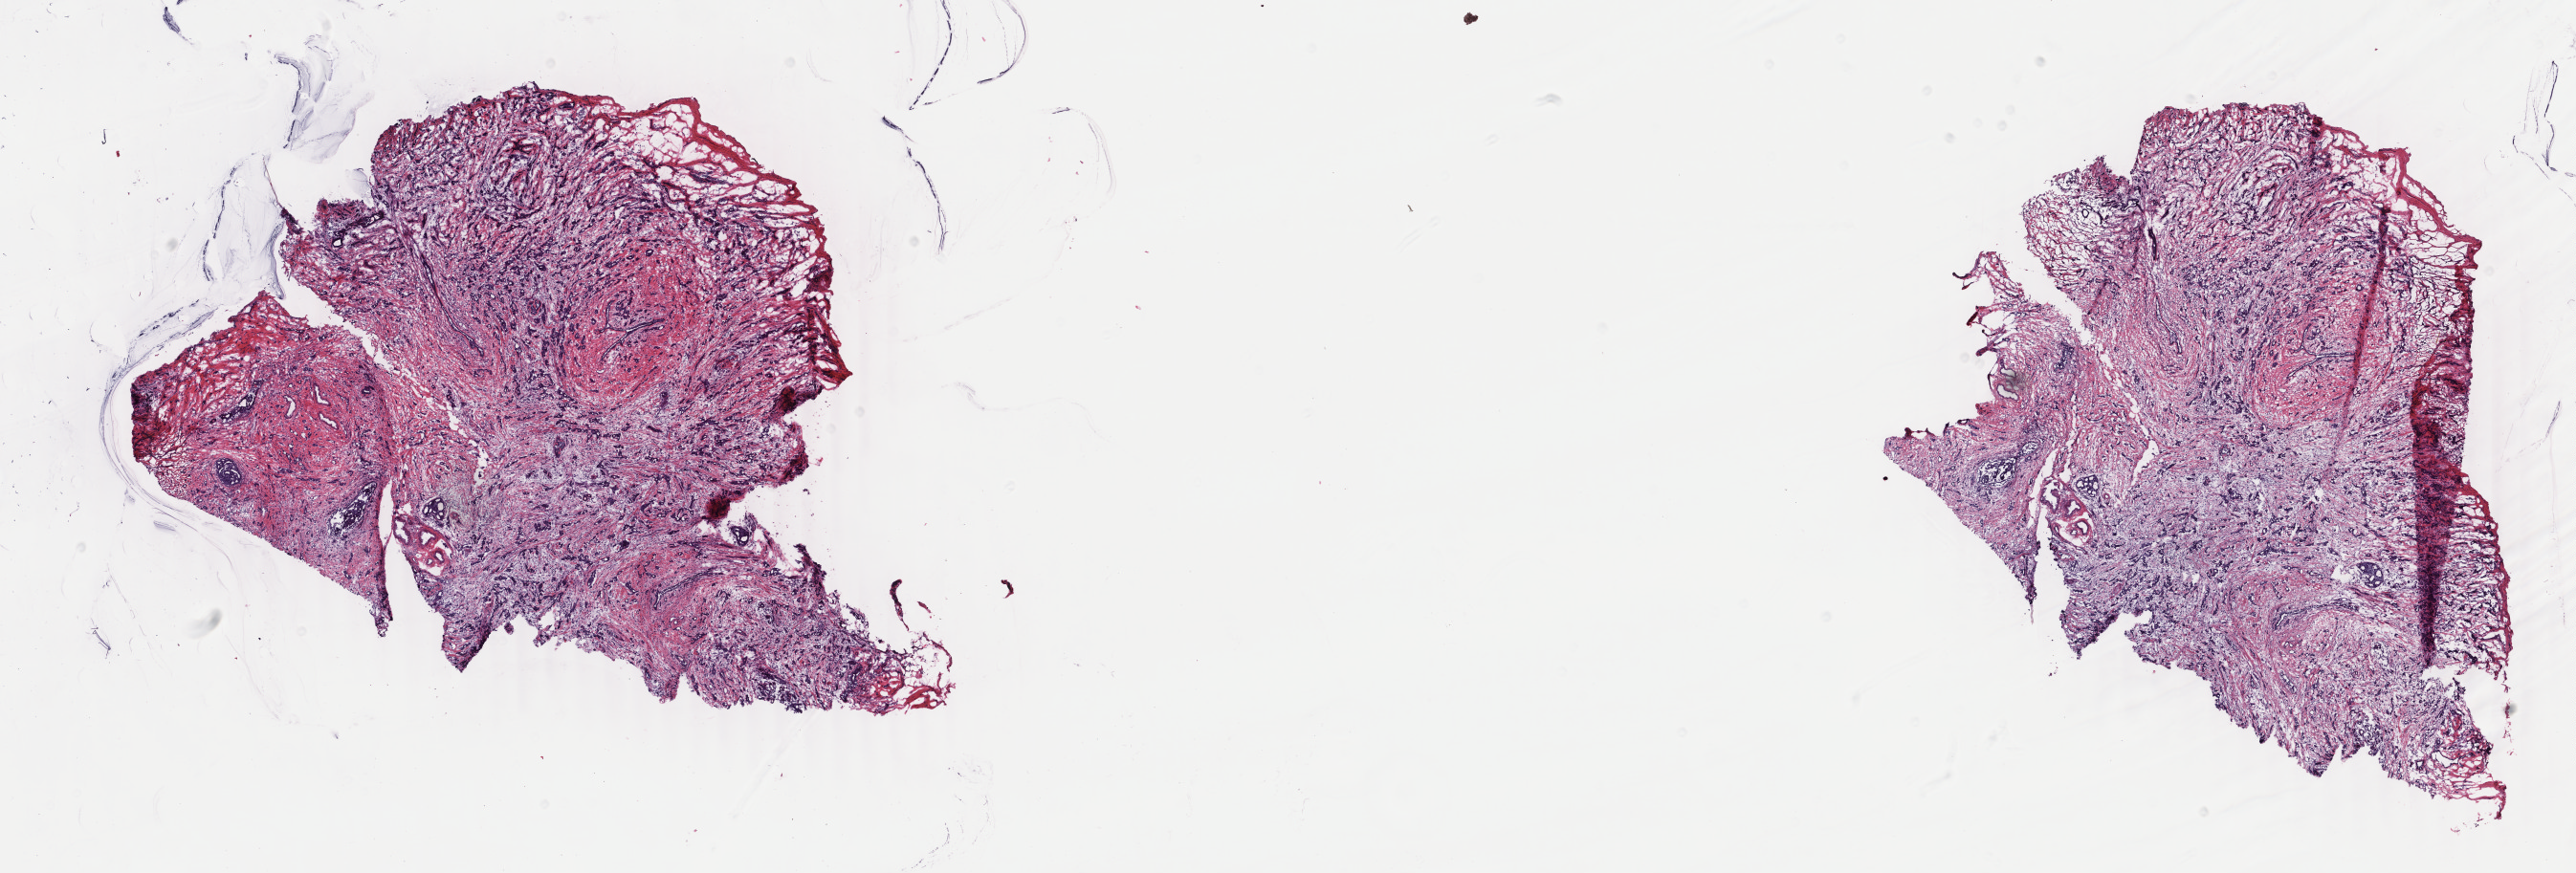
H&E-stained whole-slide image, whole scanned area (about 21.4 x 7.3 mm) shown as a low-resolution overview, frozen section from the bottom of the tissue portion, sample: primary tumour, breast. Patient: female, age at initial diagnosis 41 years. Composition of this section per pathologist review: tumour cells 70%, tumour nuclei 70%, normal cells 0%, stromal cells 20%, necrosis 10%. Inflammatory infiltration, as recorded: lymphocyte infiltration 20%, monocyte infiltration 25%, neutrophil infiltration 30%.
* AJCC pathologic stage: IIB (6th edition)
* lymph nodes positive (case pathology): 4 of 18 examined
* TNM: T2 N1a M0
* diagnosis: Infiltrating duct carcinoma, NOS